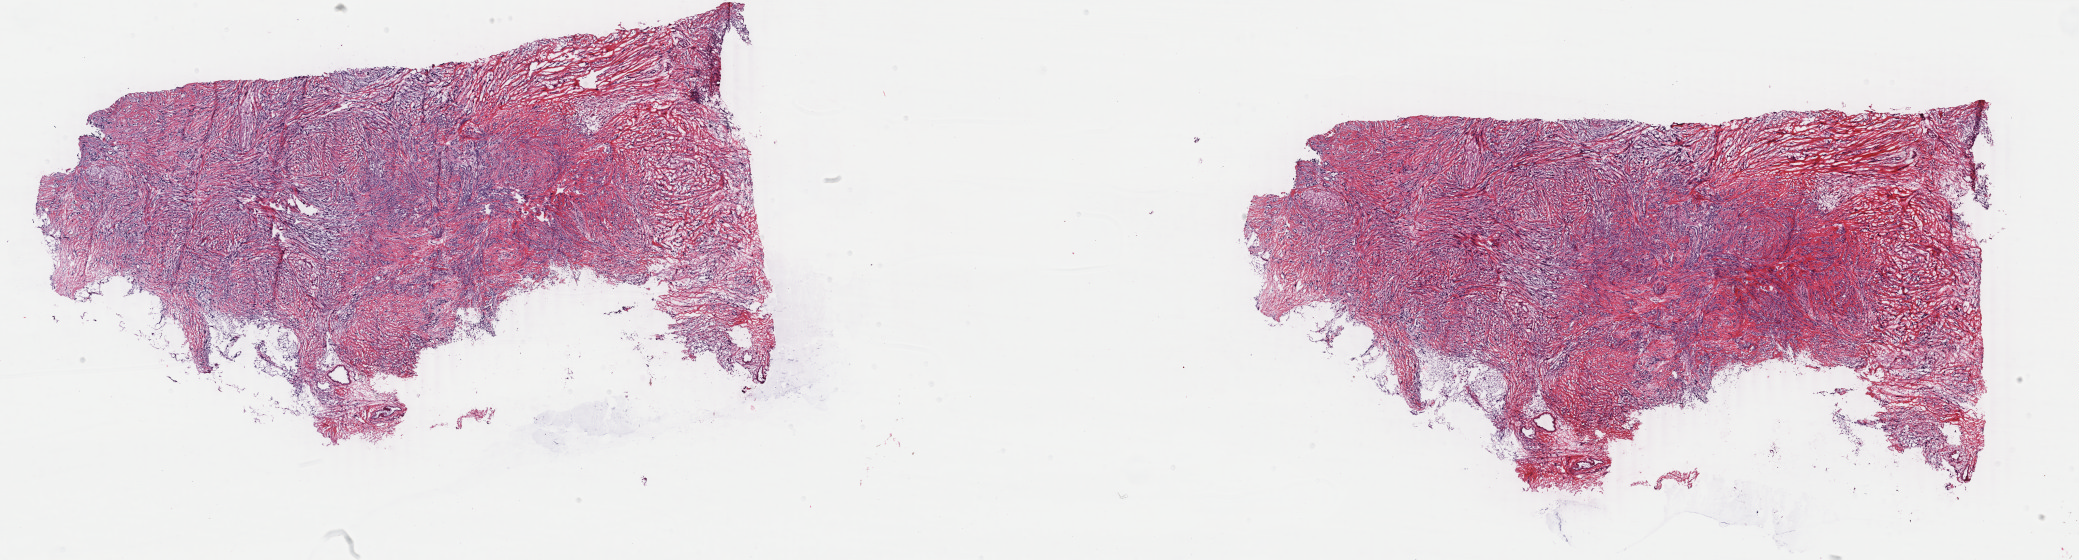
Digitized H&E tissue section (whole slide), a low-resolution overview of the entire scanned area, about 33.1 x 8.9 mm. Frozen section. Breast, primary tumour sample. Female patient; age at initial diagnosis 48 years. Pathologist review of this section (percent, as recorded): tumour cells 80%, tumour nuclei 80%, normal cells 0%, stromal cells 18%, necrosis 2%. Inflammatory infiltration, as recorded: lymphocyte infiltration 2%, monocyte infiltration 0%, neutrophil infiltration 0%.
Diagnosis: Infiltrating duct mixed with other types of carcinoma. Lymph nodes positive (case pathology): 2 of 2 examined. AJCC pathologic stage: IV.